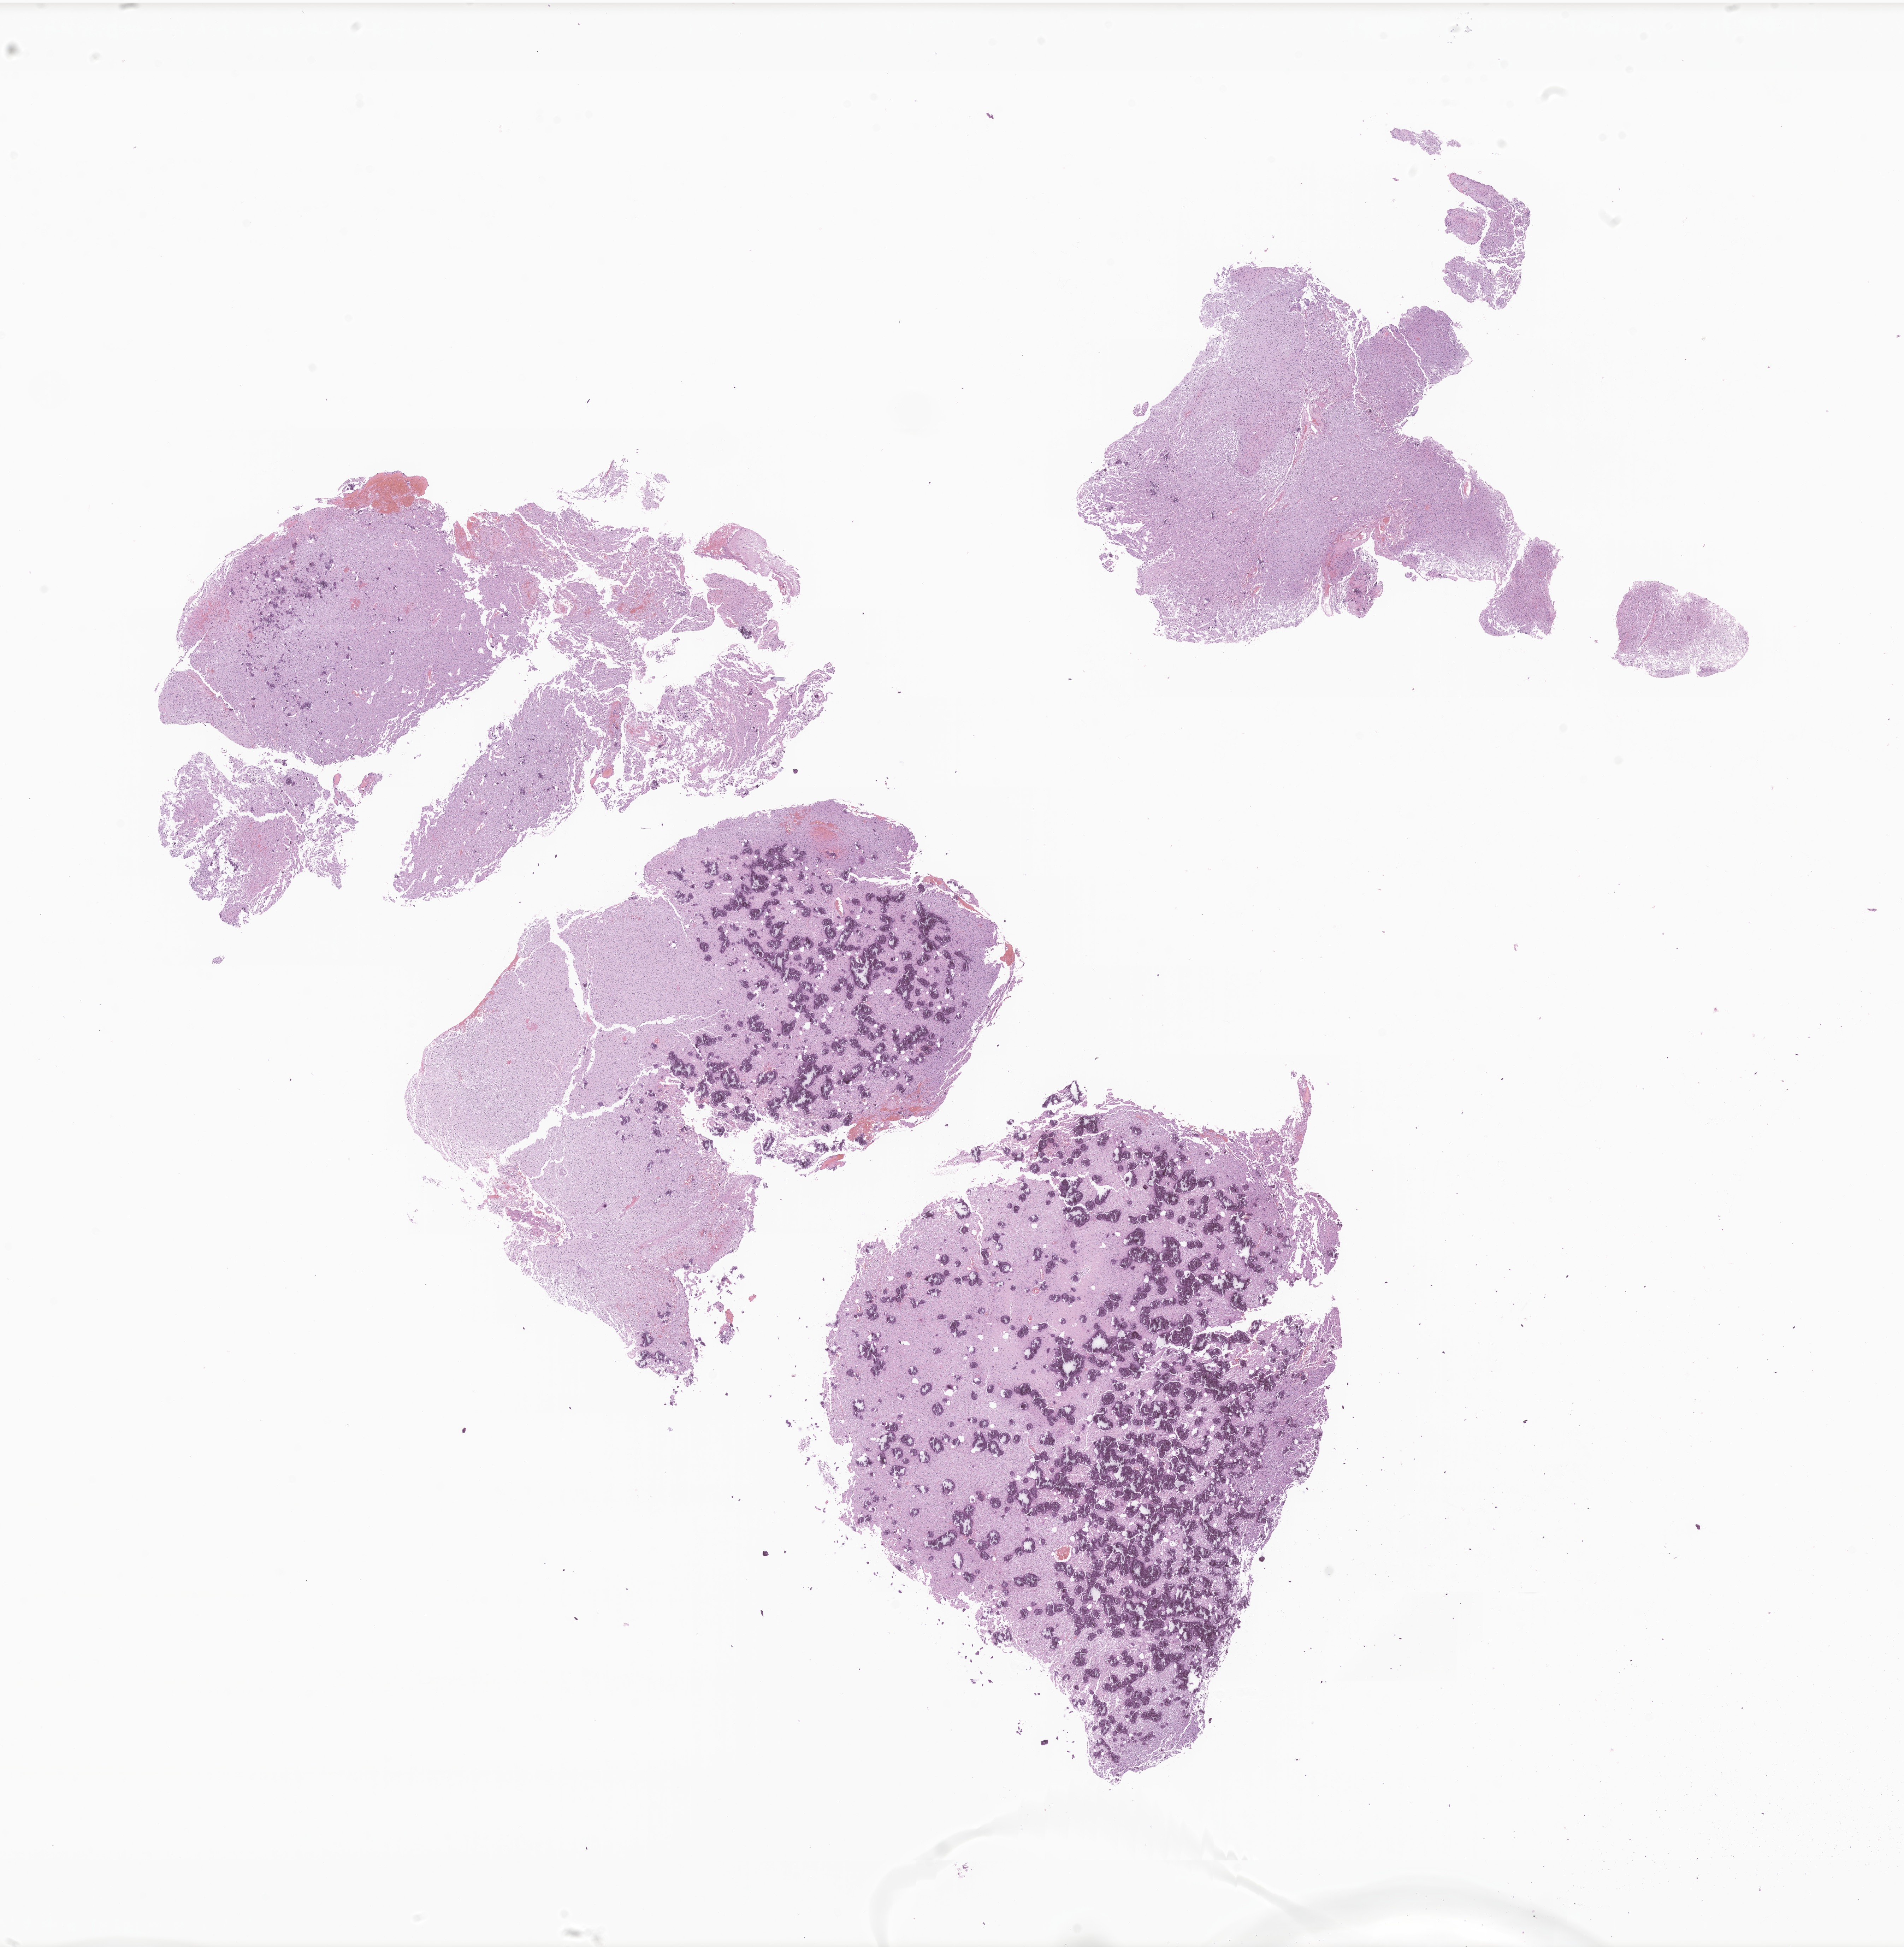
Whole-slide image, haematoxylin and eosin stain of tumor tissue from the brain — whole scanned area (about 22.7 x 23.2 mm) shown as a low-resolution overview, formalin-fixed, paraffin-embedded (FFPE) tissue. Patient: female, age 50 months (4 years 2 months).
• recorded diagnosis: Dysembryoplastic neuroepithelial tumor